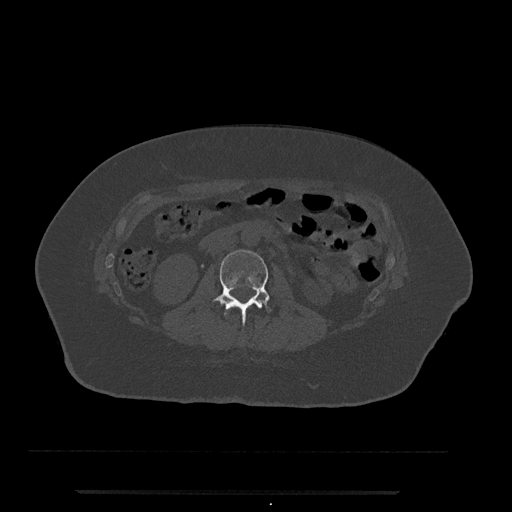
CT including the spine, one axial slice. Position 36 of 797 along the scan axis. 120 kVp. Bone window (W 1800 / L 400 HU). 0.5 mm slice thickness. 512 × 512 image matrix, field of view 440 × 440 mm. Female patient, age 51 years. From the clinical record (not read from this slice): primary cancer: neuro; vertebrae with lytic lesions (as recorded): T8.
Outlined on this slice (semi-automatically segmented with operator editing):
- L2 vertebra: bounding box (x1, y1, x2, y2) in pixels: (212, 250, 271, 323)